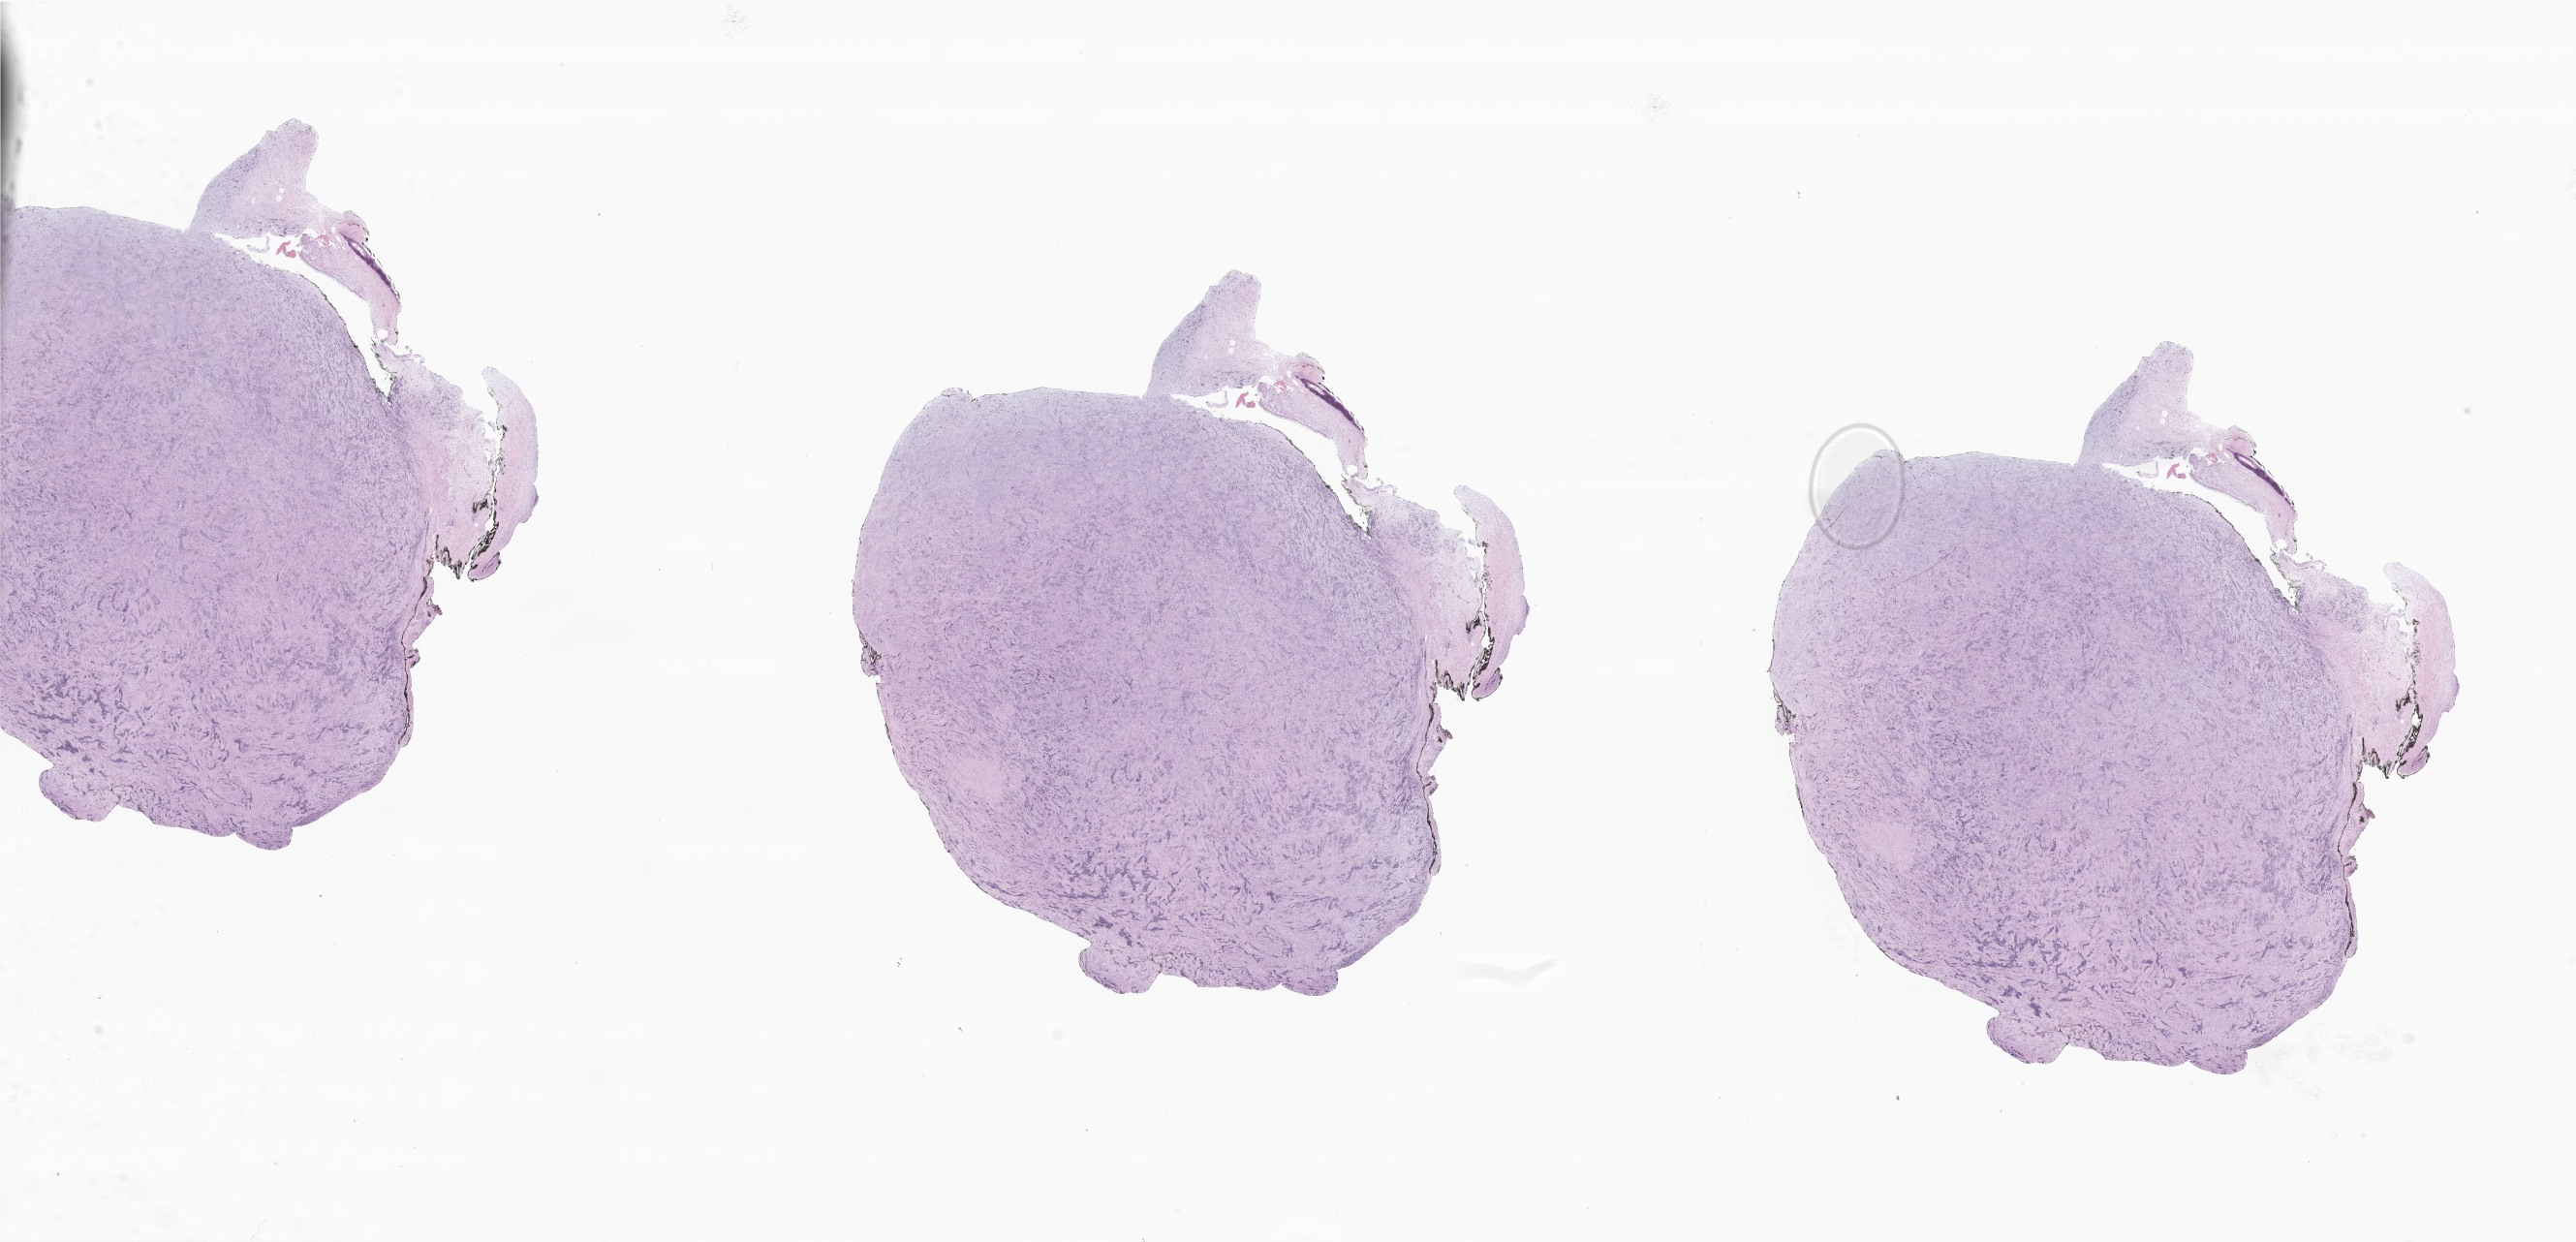
Whole-slide image, haematoxylin and eosin stain of tumor tissue from the upper gum — low-resolution overview of the scanned area, about 44.8 x 21.6 mm; FFPE section. Patient female; age 185 days.
Diagnosis: Melanotic neuroectodermal tumor.